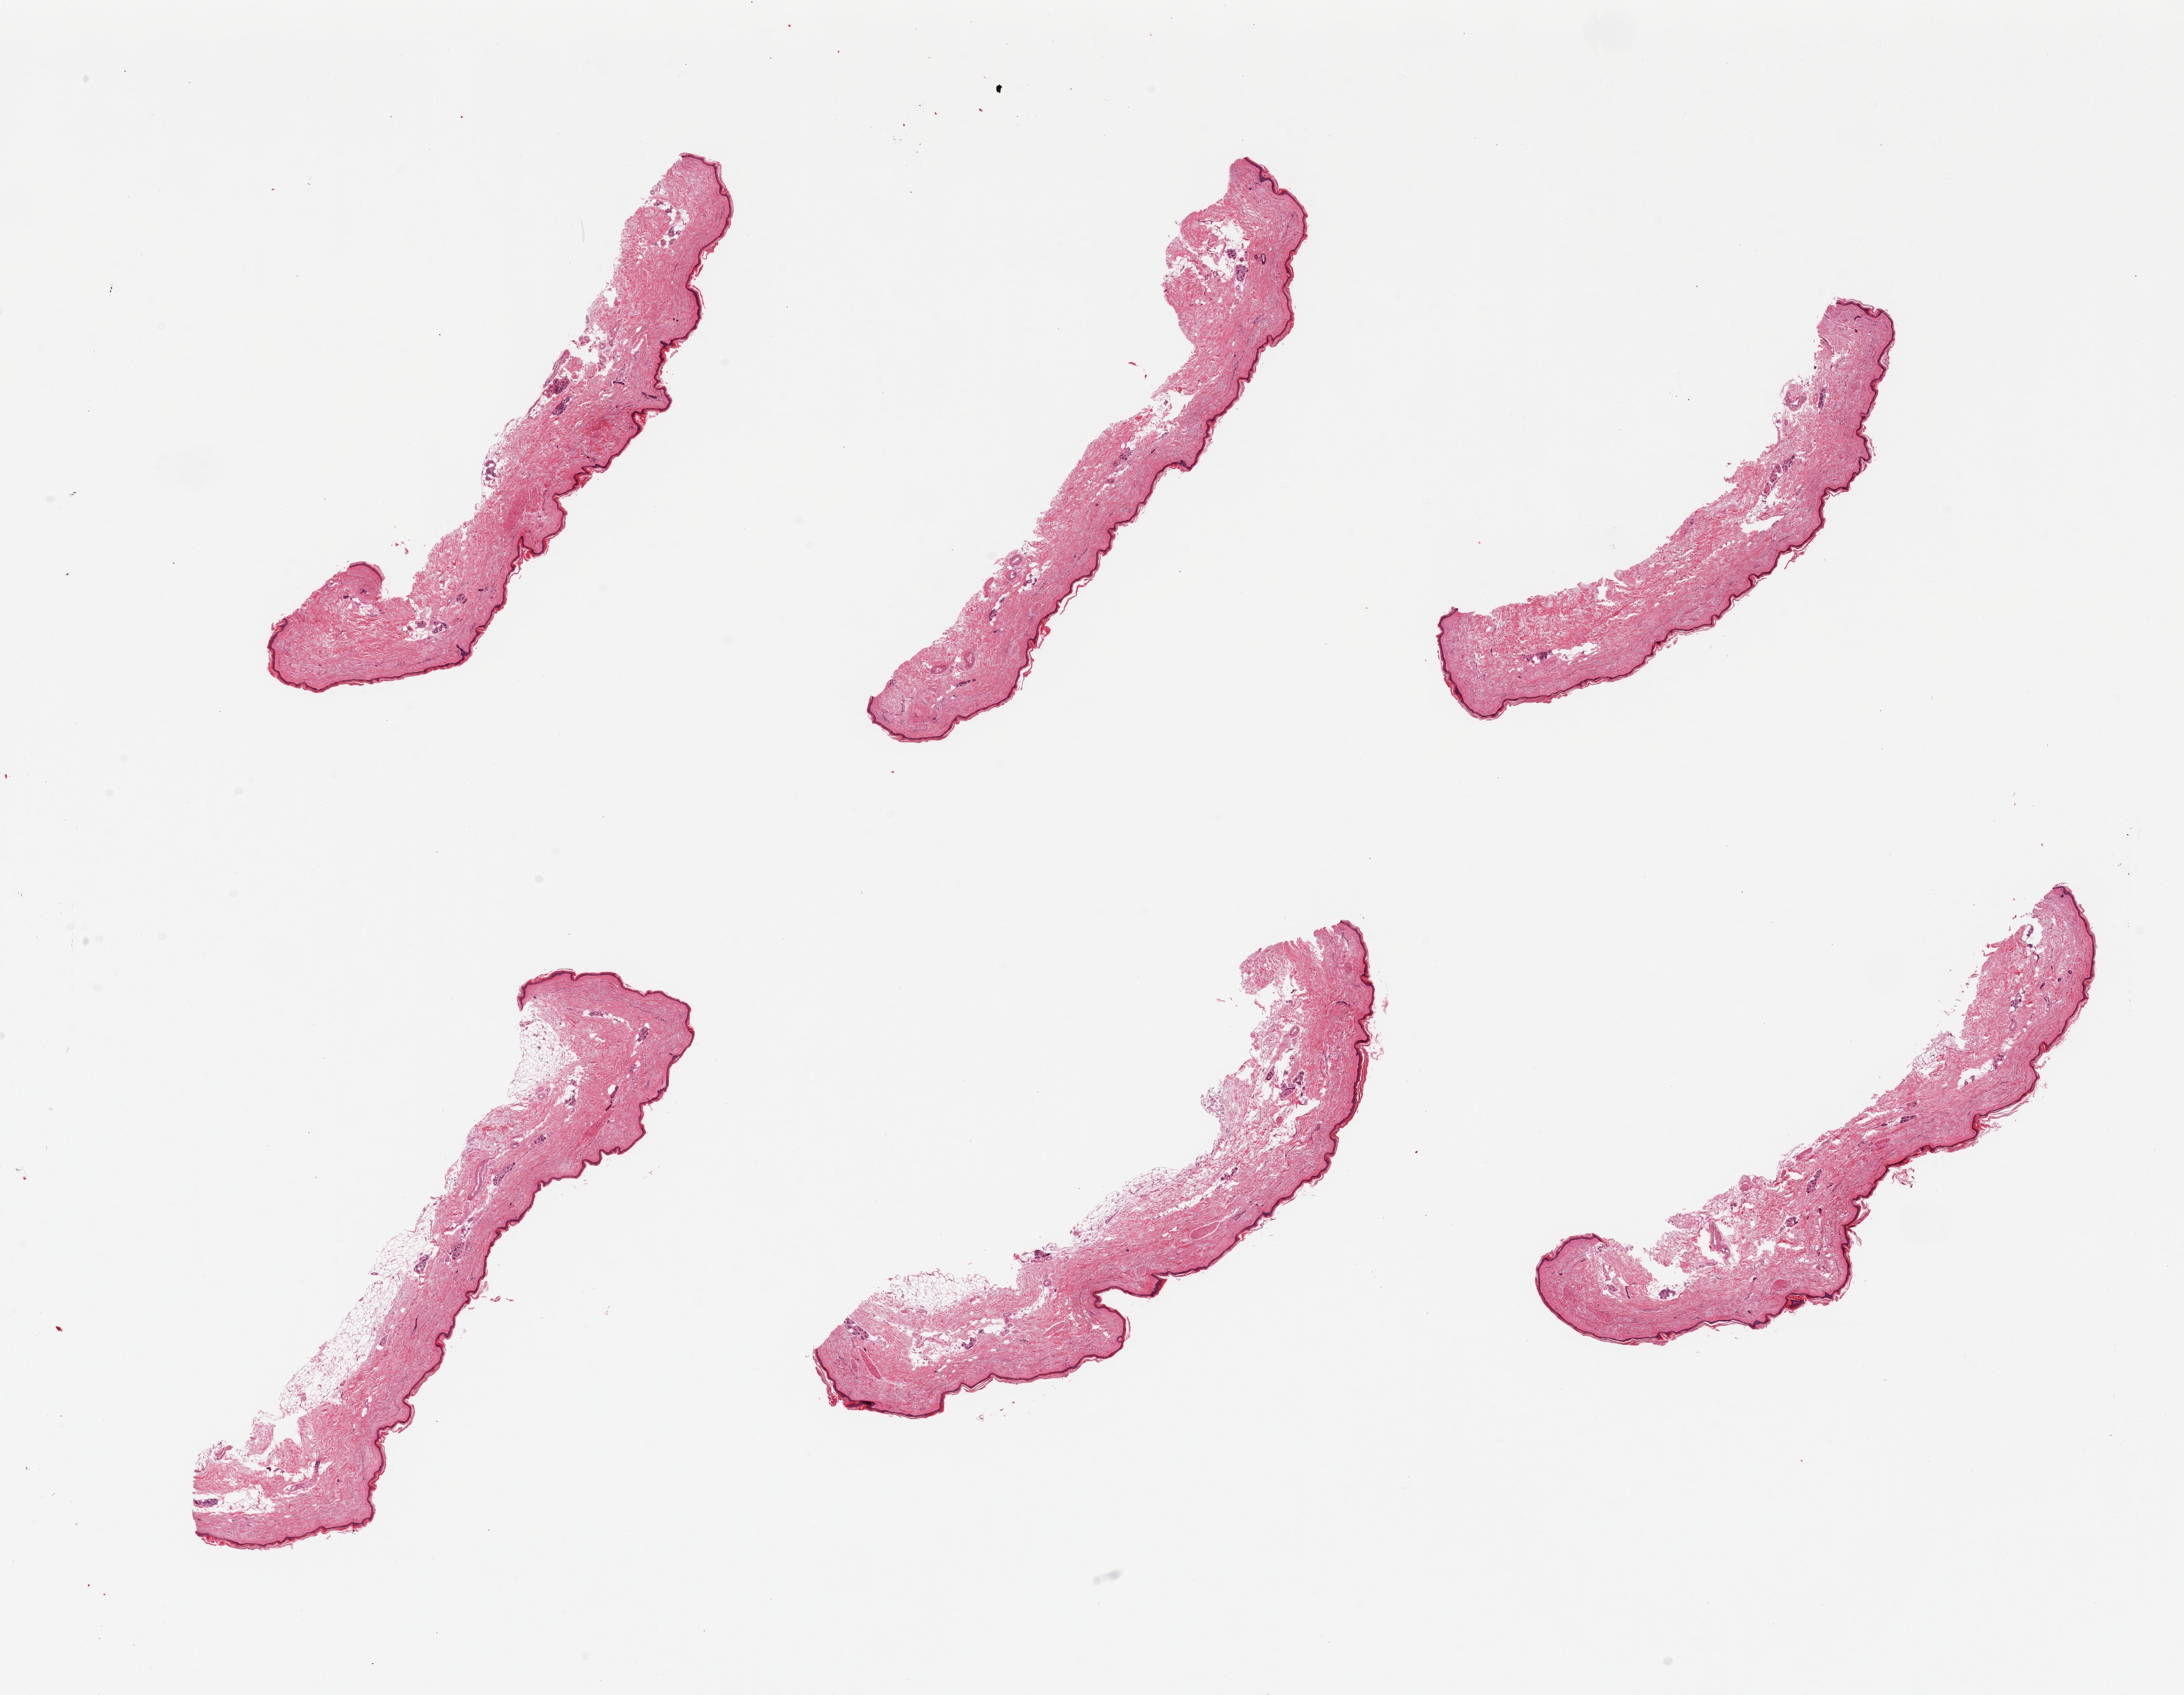
H&E whole-slide image — whole scanned area (about 25.6 x 19.9 mm) shown as a low-resolution overview, PAXgene-fixed, paraffin-embedded tissue, sampled site (target tissue): skin of lower leg, tissue donor sample. Donor sex: female.
Review note (as recorded): 6 pieces, trace dermal fat up to ~0.5mm; squamous epithelium atrophic, ~10-30 microns.